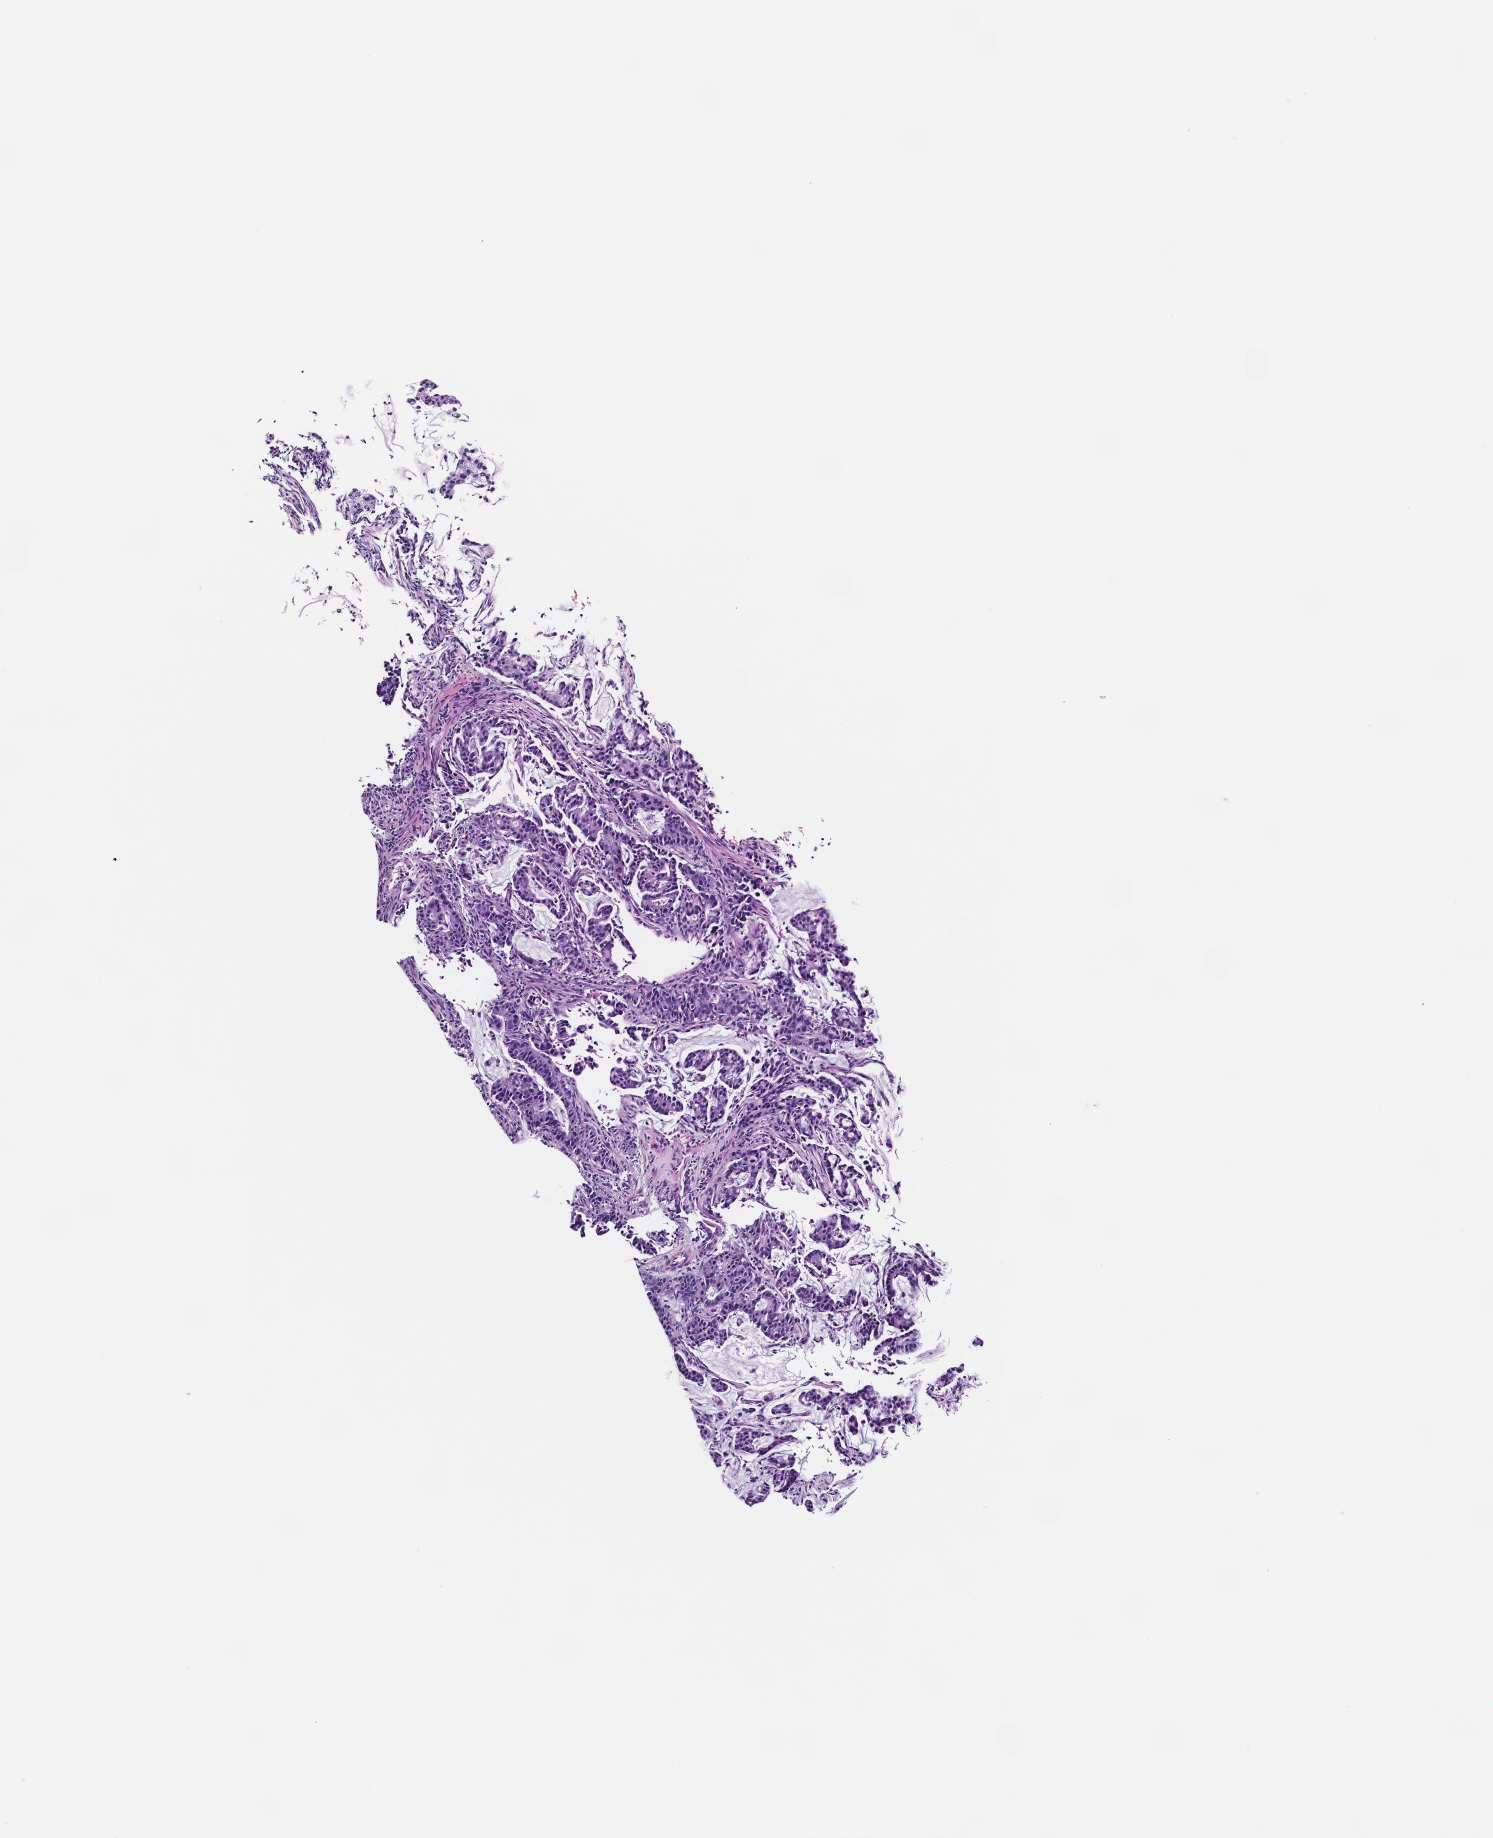
Whole-slide image, hematoxylin and eosin (H&E) stain — whole scanned area (about 3.0 x 3.7 mm) shown as a low-resolution overview. Formalin-fixed, paraffin-embedded (FFPE) tissue. Patient: male.
• this section: metastatic tumor tissue
• patient diagnosis (primary): Adenocarcinoma of the Gastroesophageal Junction